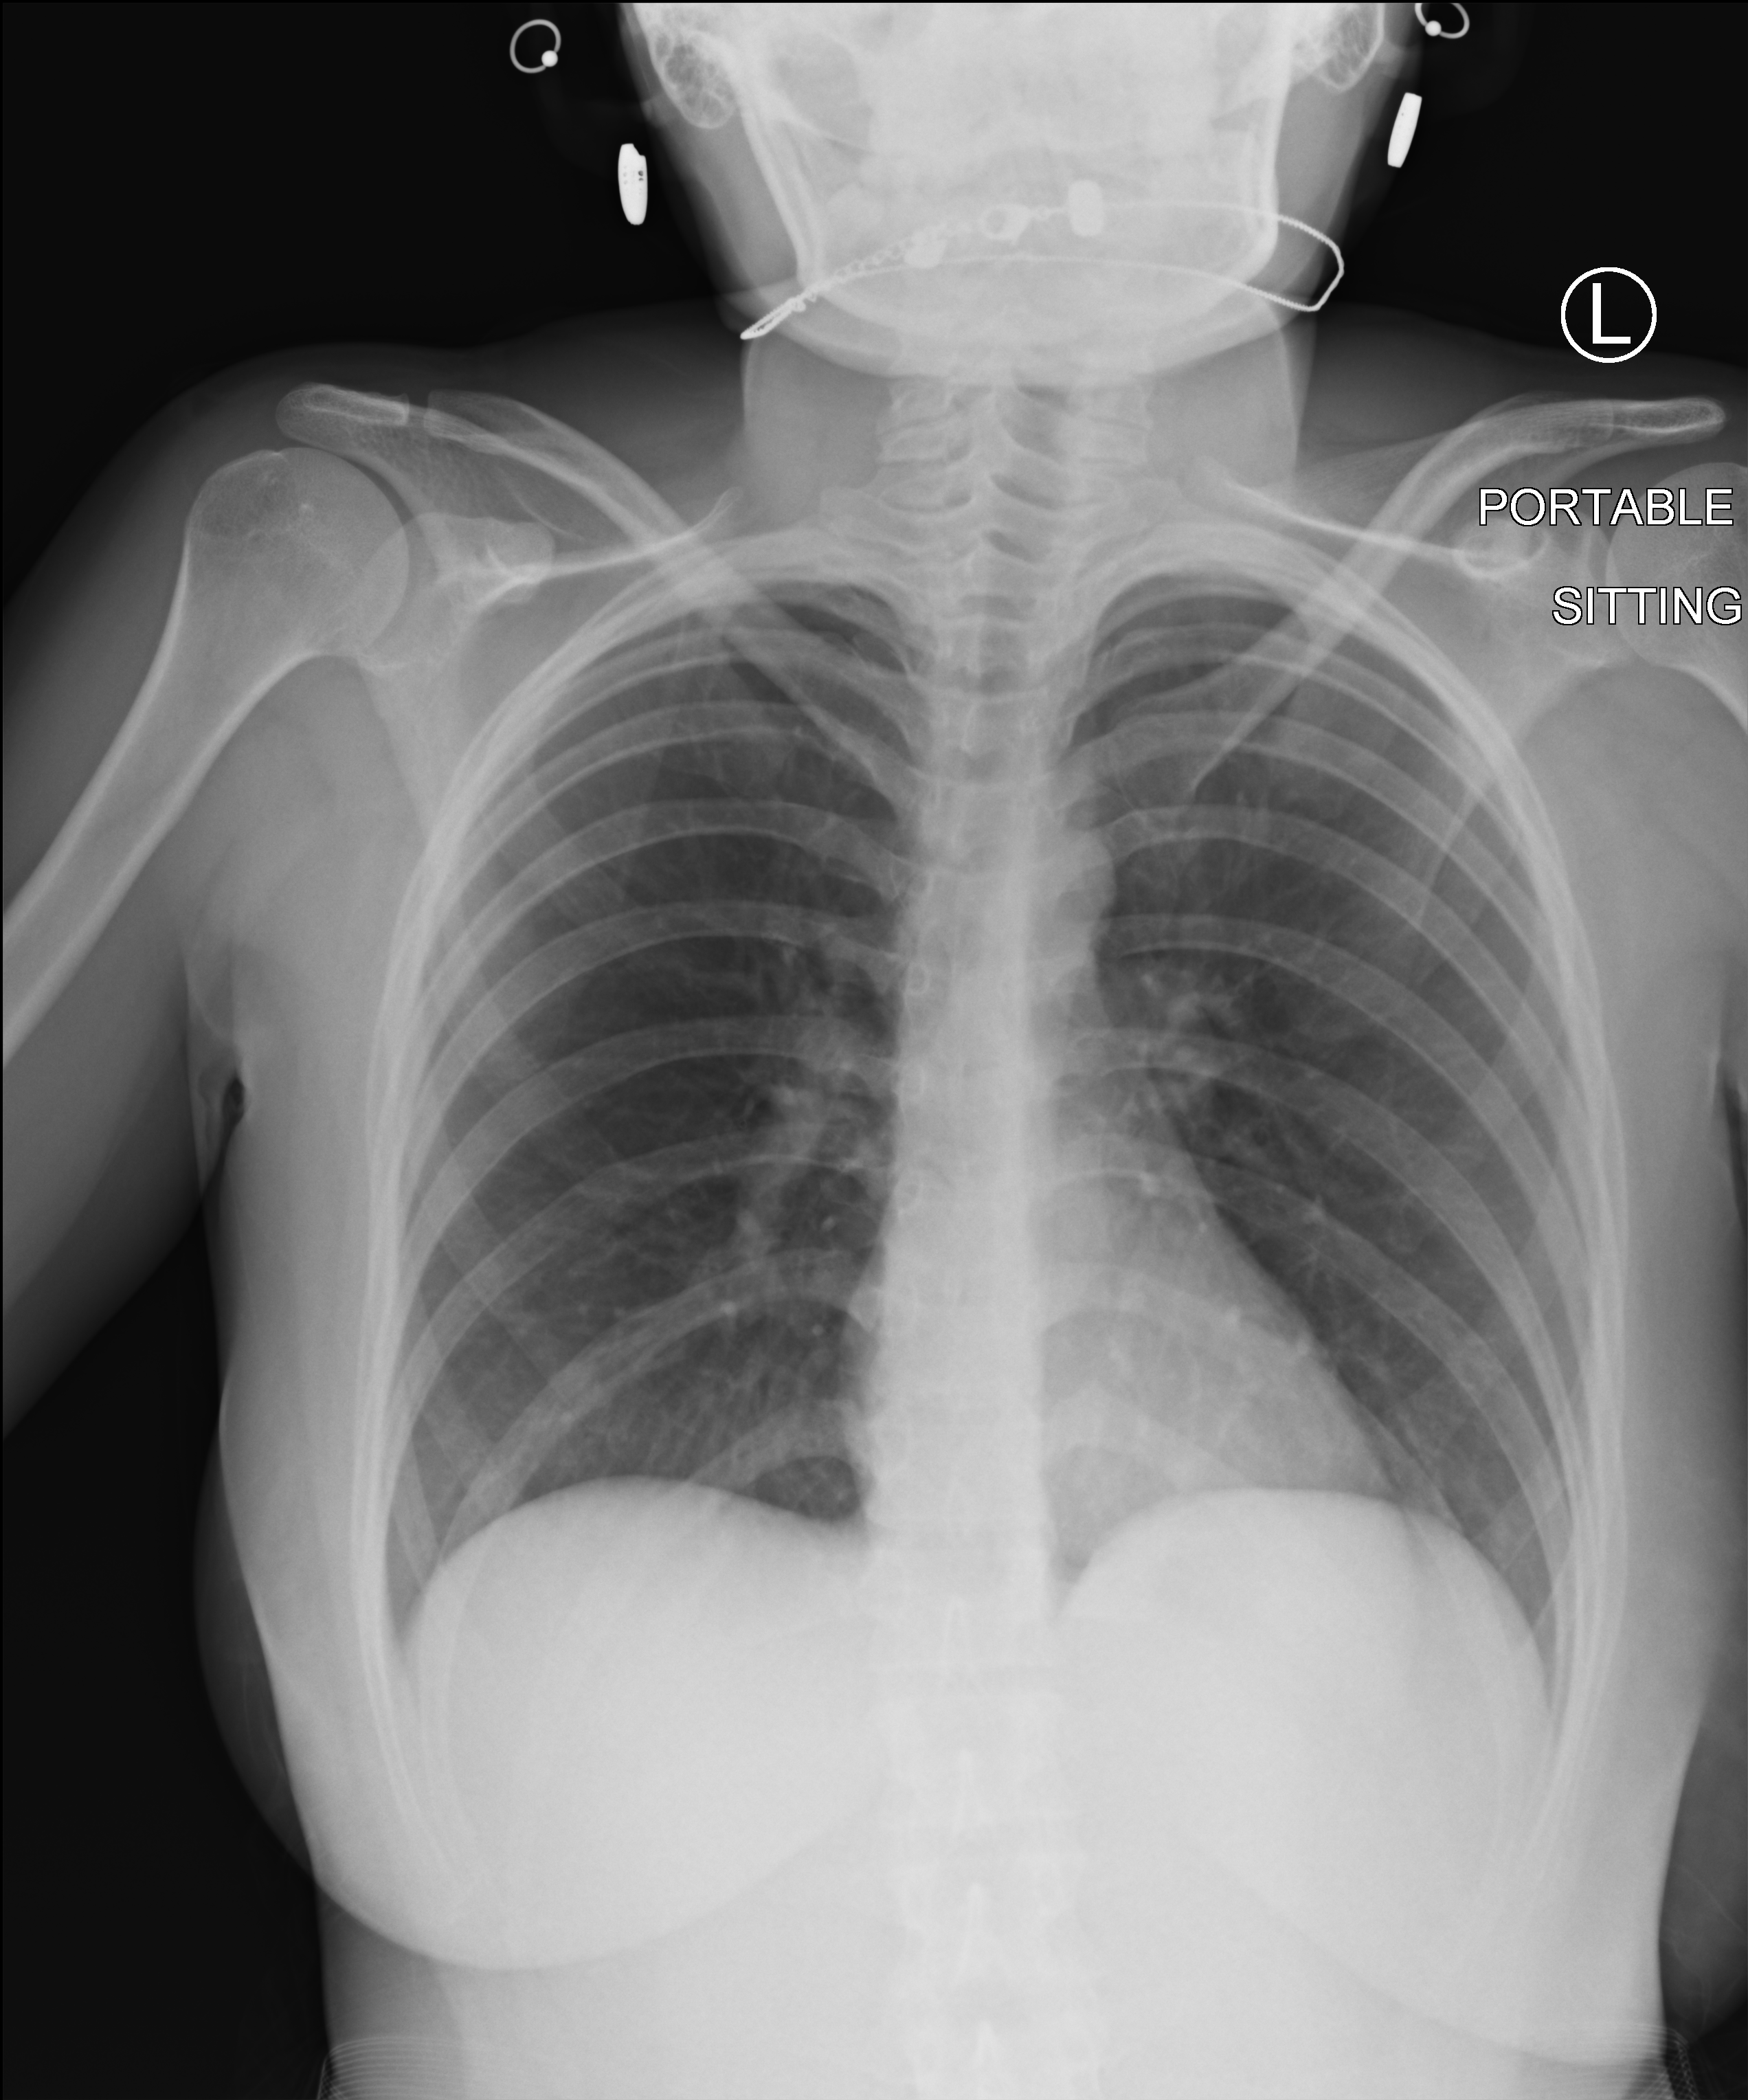
Bedside chest radiograph (computed radiography), anteroposterior (AP) projection. Patient hospitalised with COVID-19; female, aged 18–59 years.
Hospital-stay facts (about this admission, not read from this image; timing relative to this image not recorded):
- admitted to intensive care during this hospital stay: no
- mechanically ventilated during this hospital stay: no